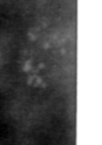
Crop from a digitized film mammogram around one marked abnormality, left breast, MLO view.
Finding: calcifications, morphology pleomorphic, distribution clustered; BI-RADS assessment category 4; pathology result (as recorded, not read from the image): benign.